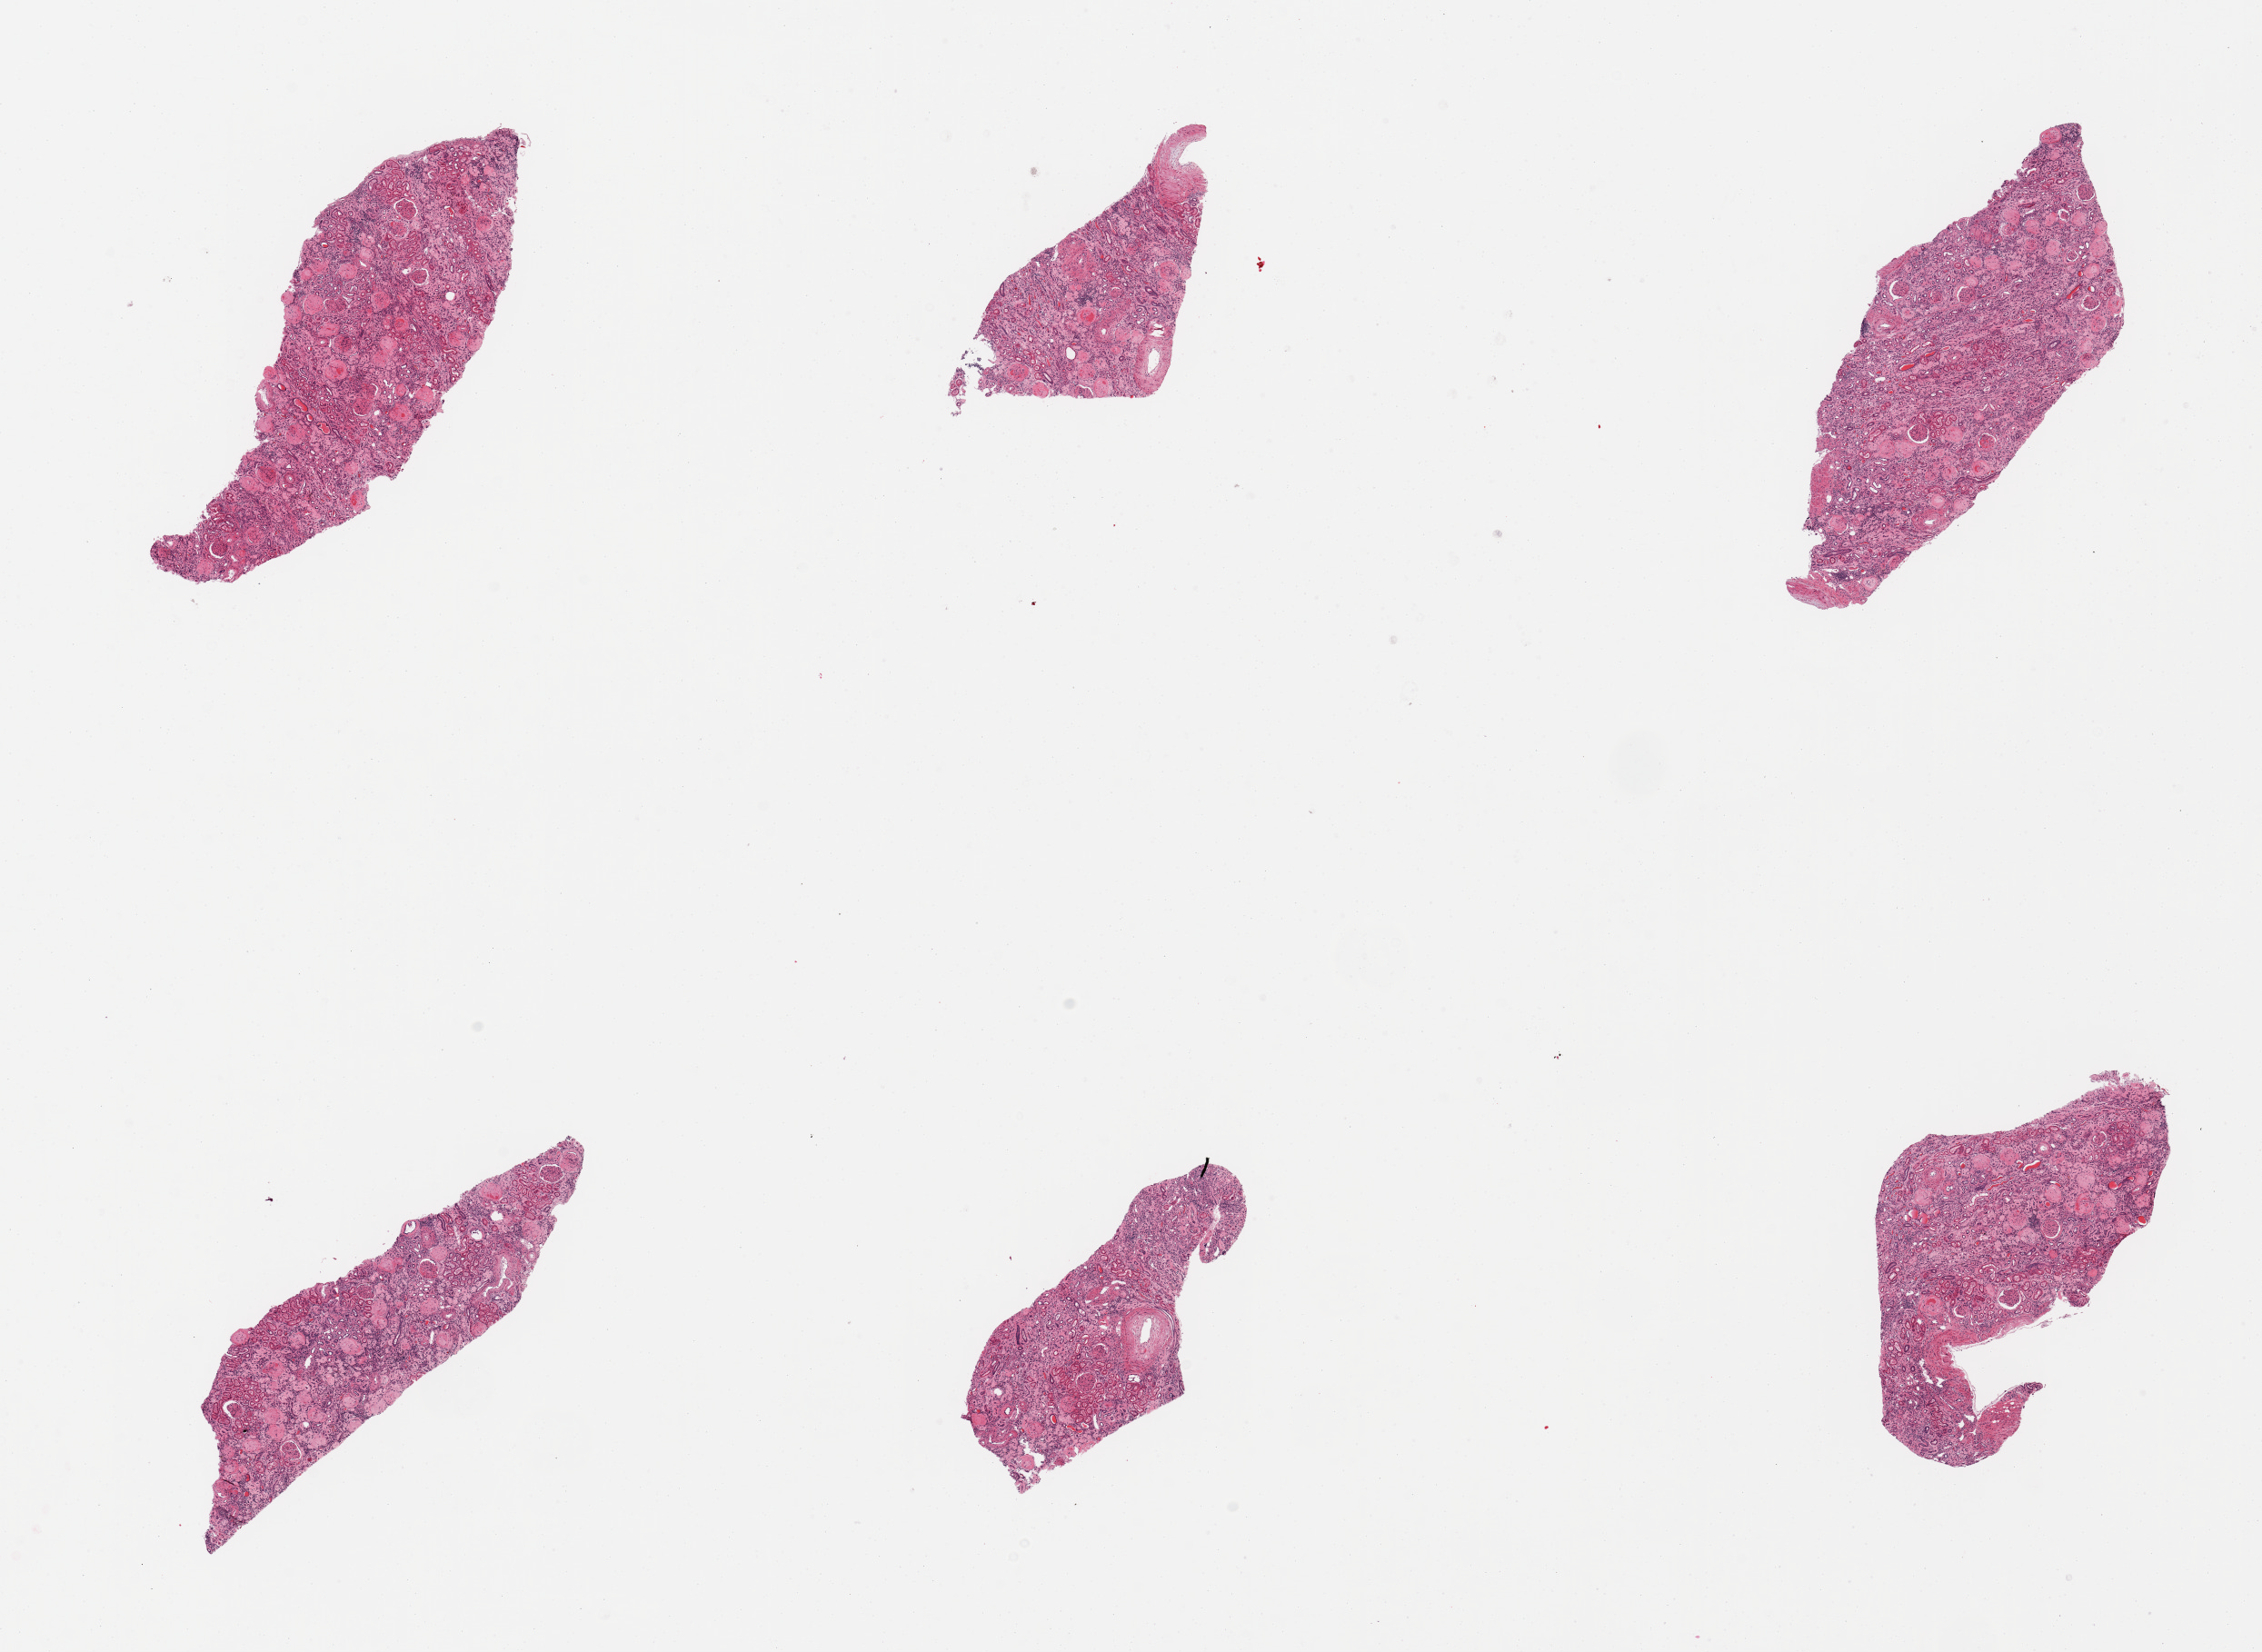
Whole-slide image, haematoxylin and eosin stain — a low-resolution overview of the entire scanned area, about 19.7 x 14.4 mm, PAXgene-fixed, paraffin-embedded tissue, sampled site (target tissue): renal cortex, tissue donor sample. Donor sex: male.
- review note (as recorded): 6 pieces; advanced arterio and arteriolonephrosclerosis with hyalinized glomeruli and chronic nephritis; end stage renal disease, diabetic glomerulosclerosis